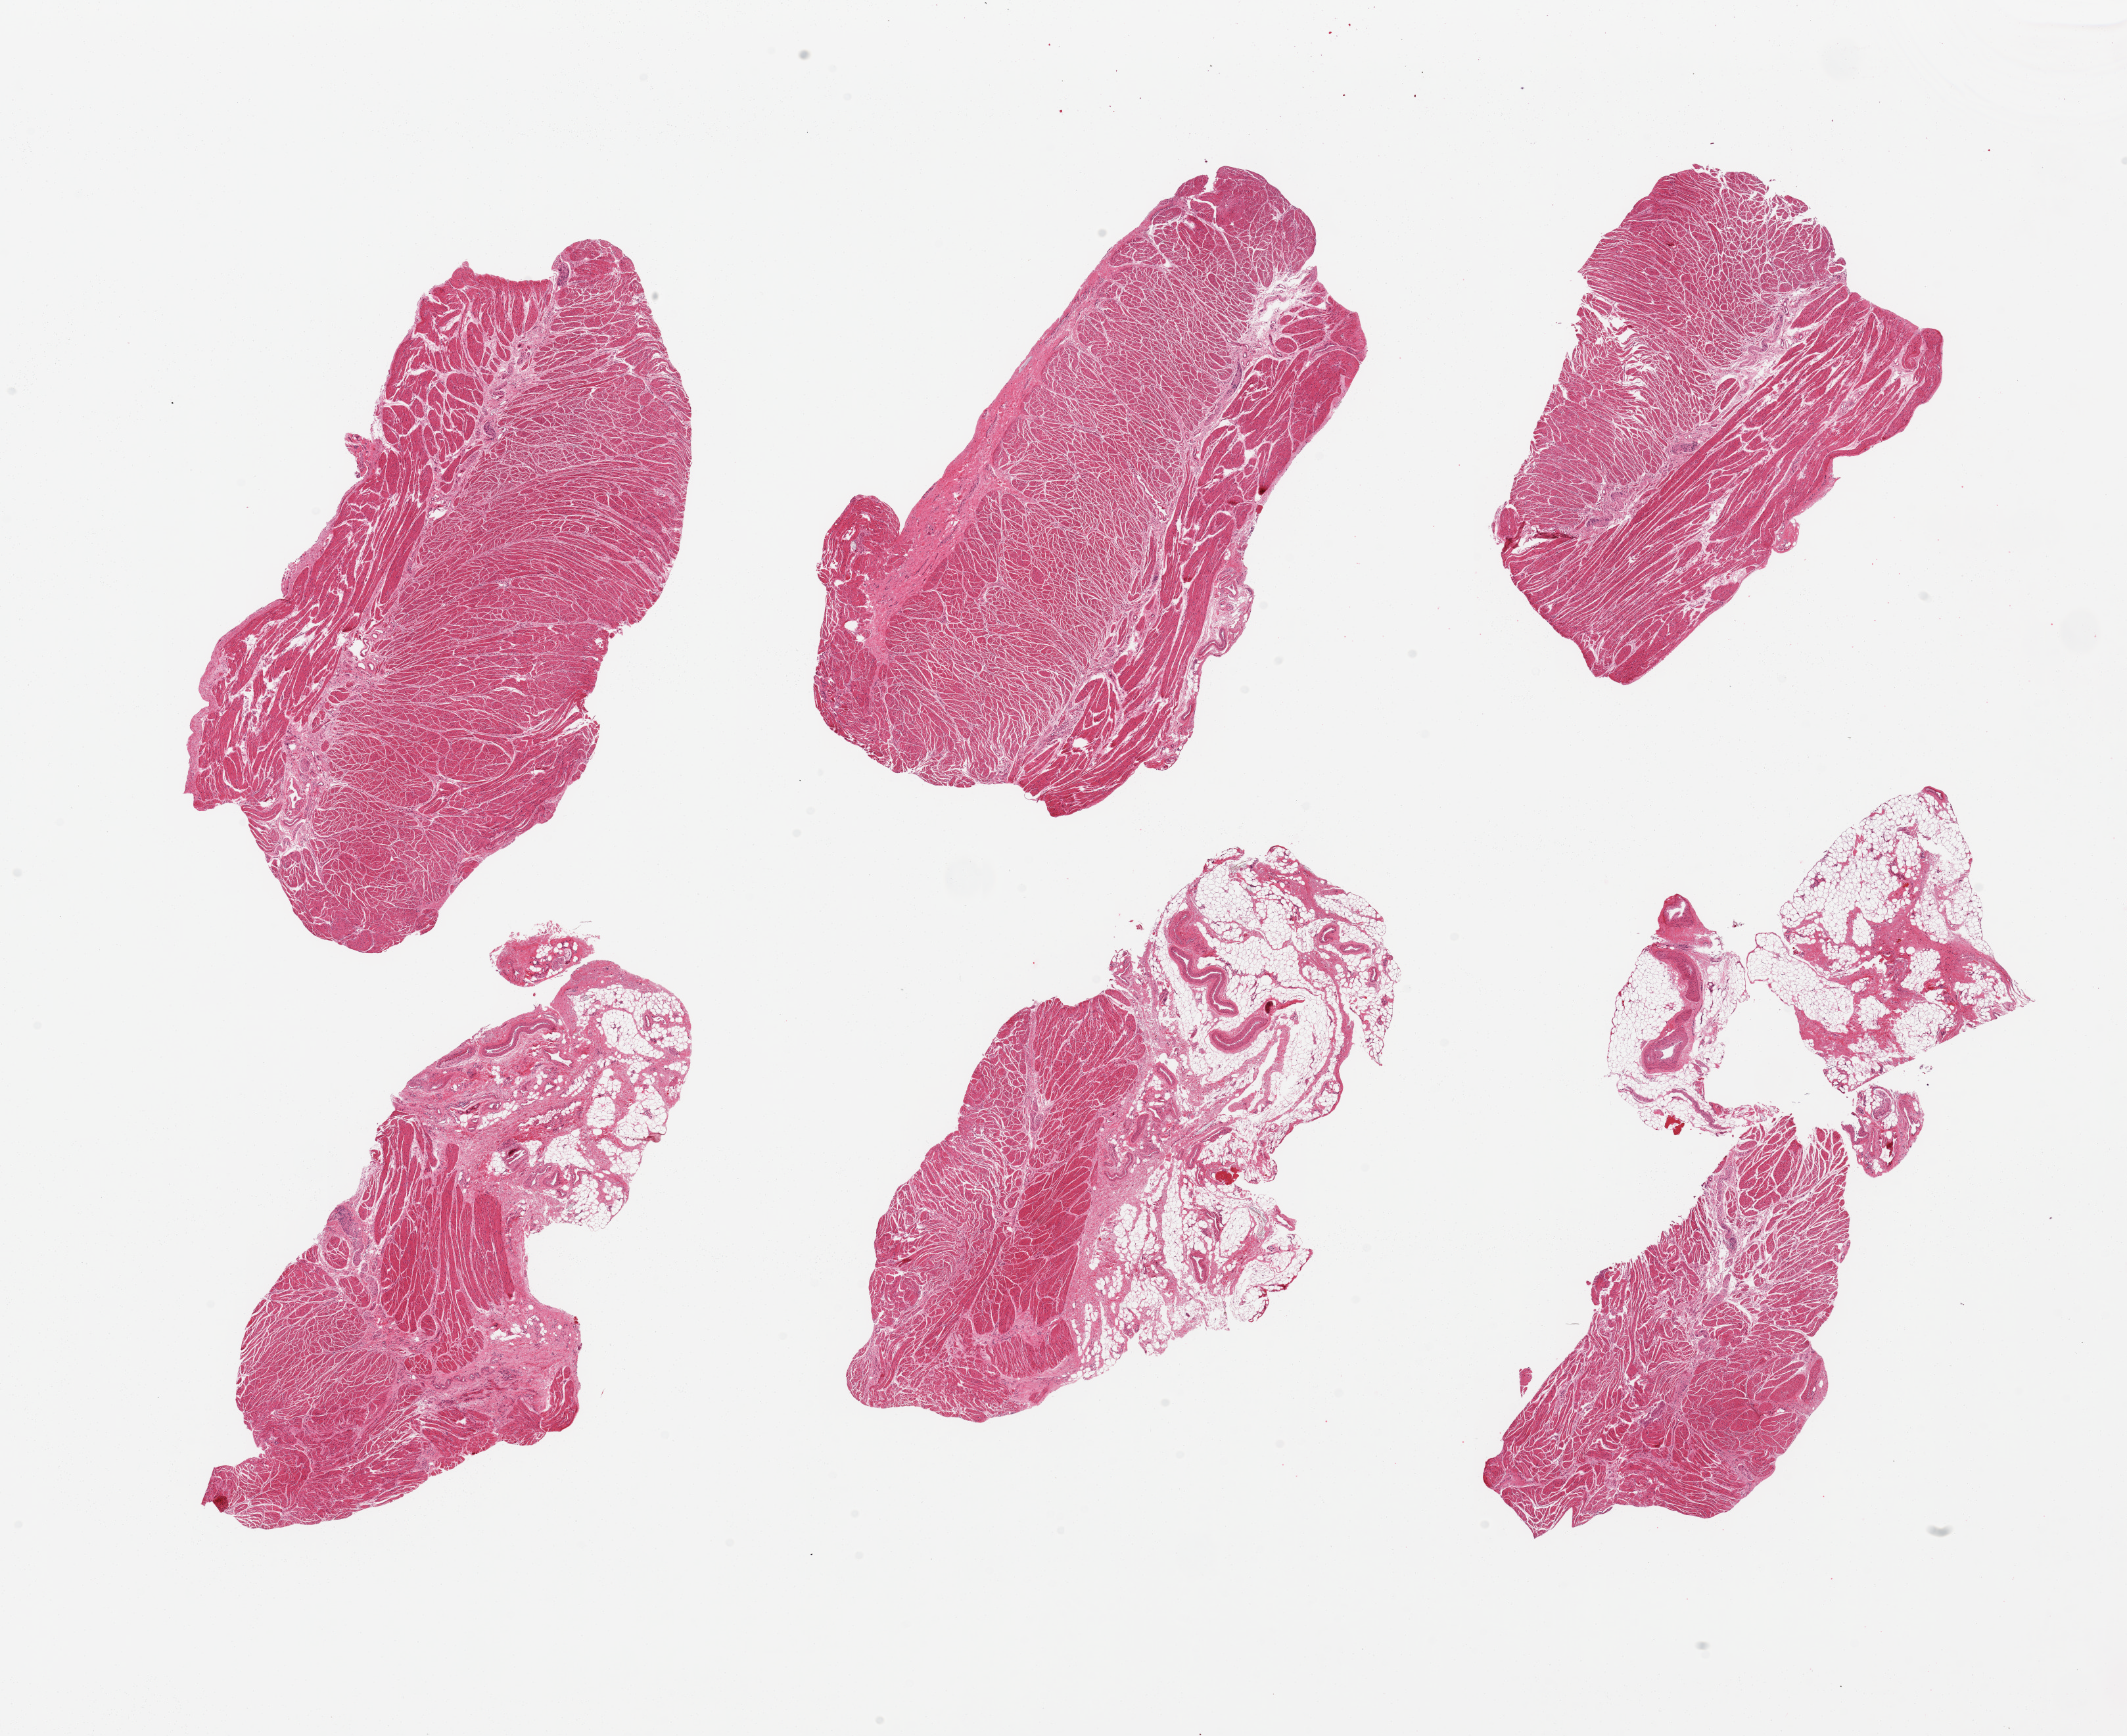
H&E whole-slide image — low-resolution overview of the scanned area, about 25.6 x 20.9 mm, PAXgene-fixed paraffin-embedded (PFPE) section, section of gastroesophageal junction (target tissue), donor tissue sample. Donor sex: female.
Review note (as recorded): 6 pieces, 3 of which have 50% extraneous fibrovascular & fatty tissue.